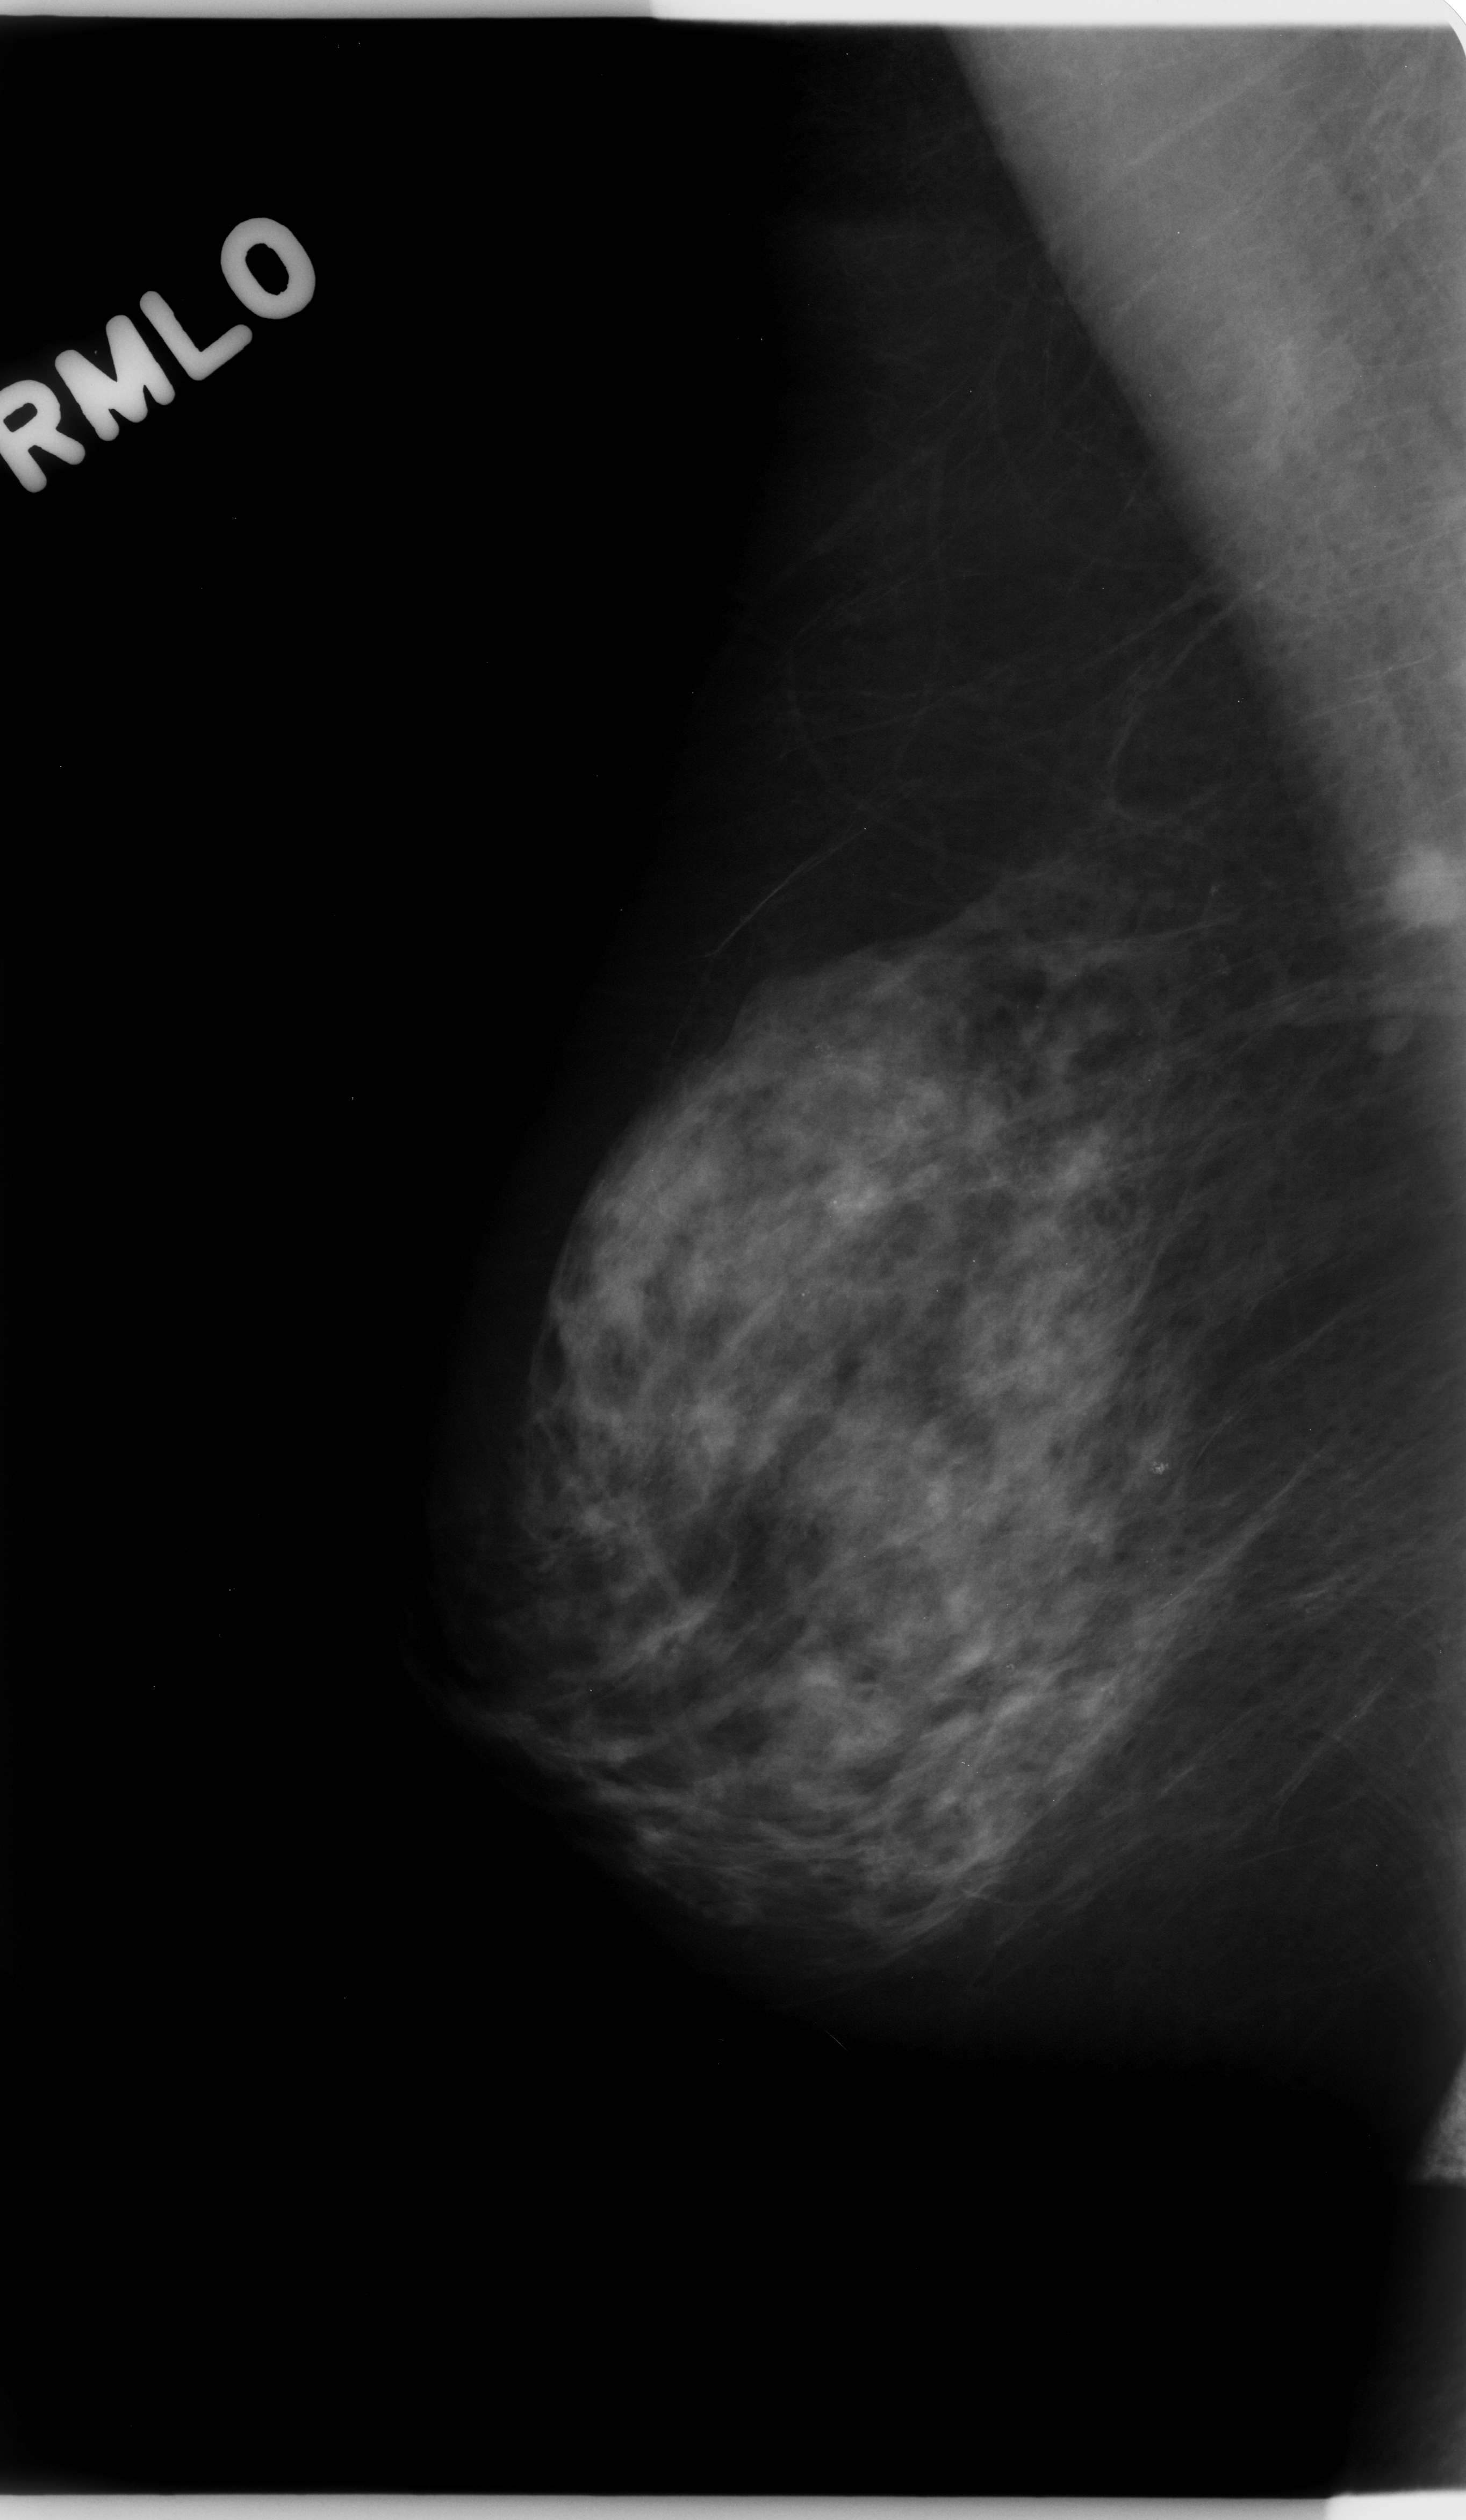
Scanned film-screen mammogram. Right breast. MLO view. 1466 × 2520 image matrix.
Expert-marked regions of interest on this film, with their recorded descriptors:
- mass, shape round, margins microlobulated; BI-RADS assessment category 5; subtlety rating 5 on a 1 (subtle) to 5 (obvious) scale; pathology (as recorded): malignant: bounding box (x1, y1, x2, y2) in pixels: (1349, 829, 1466, 946)